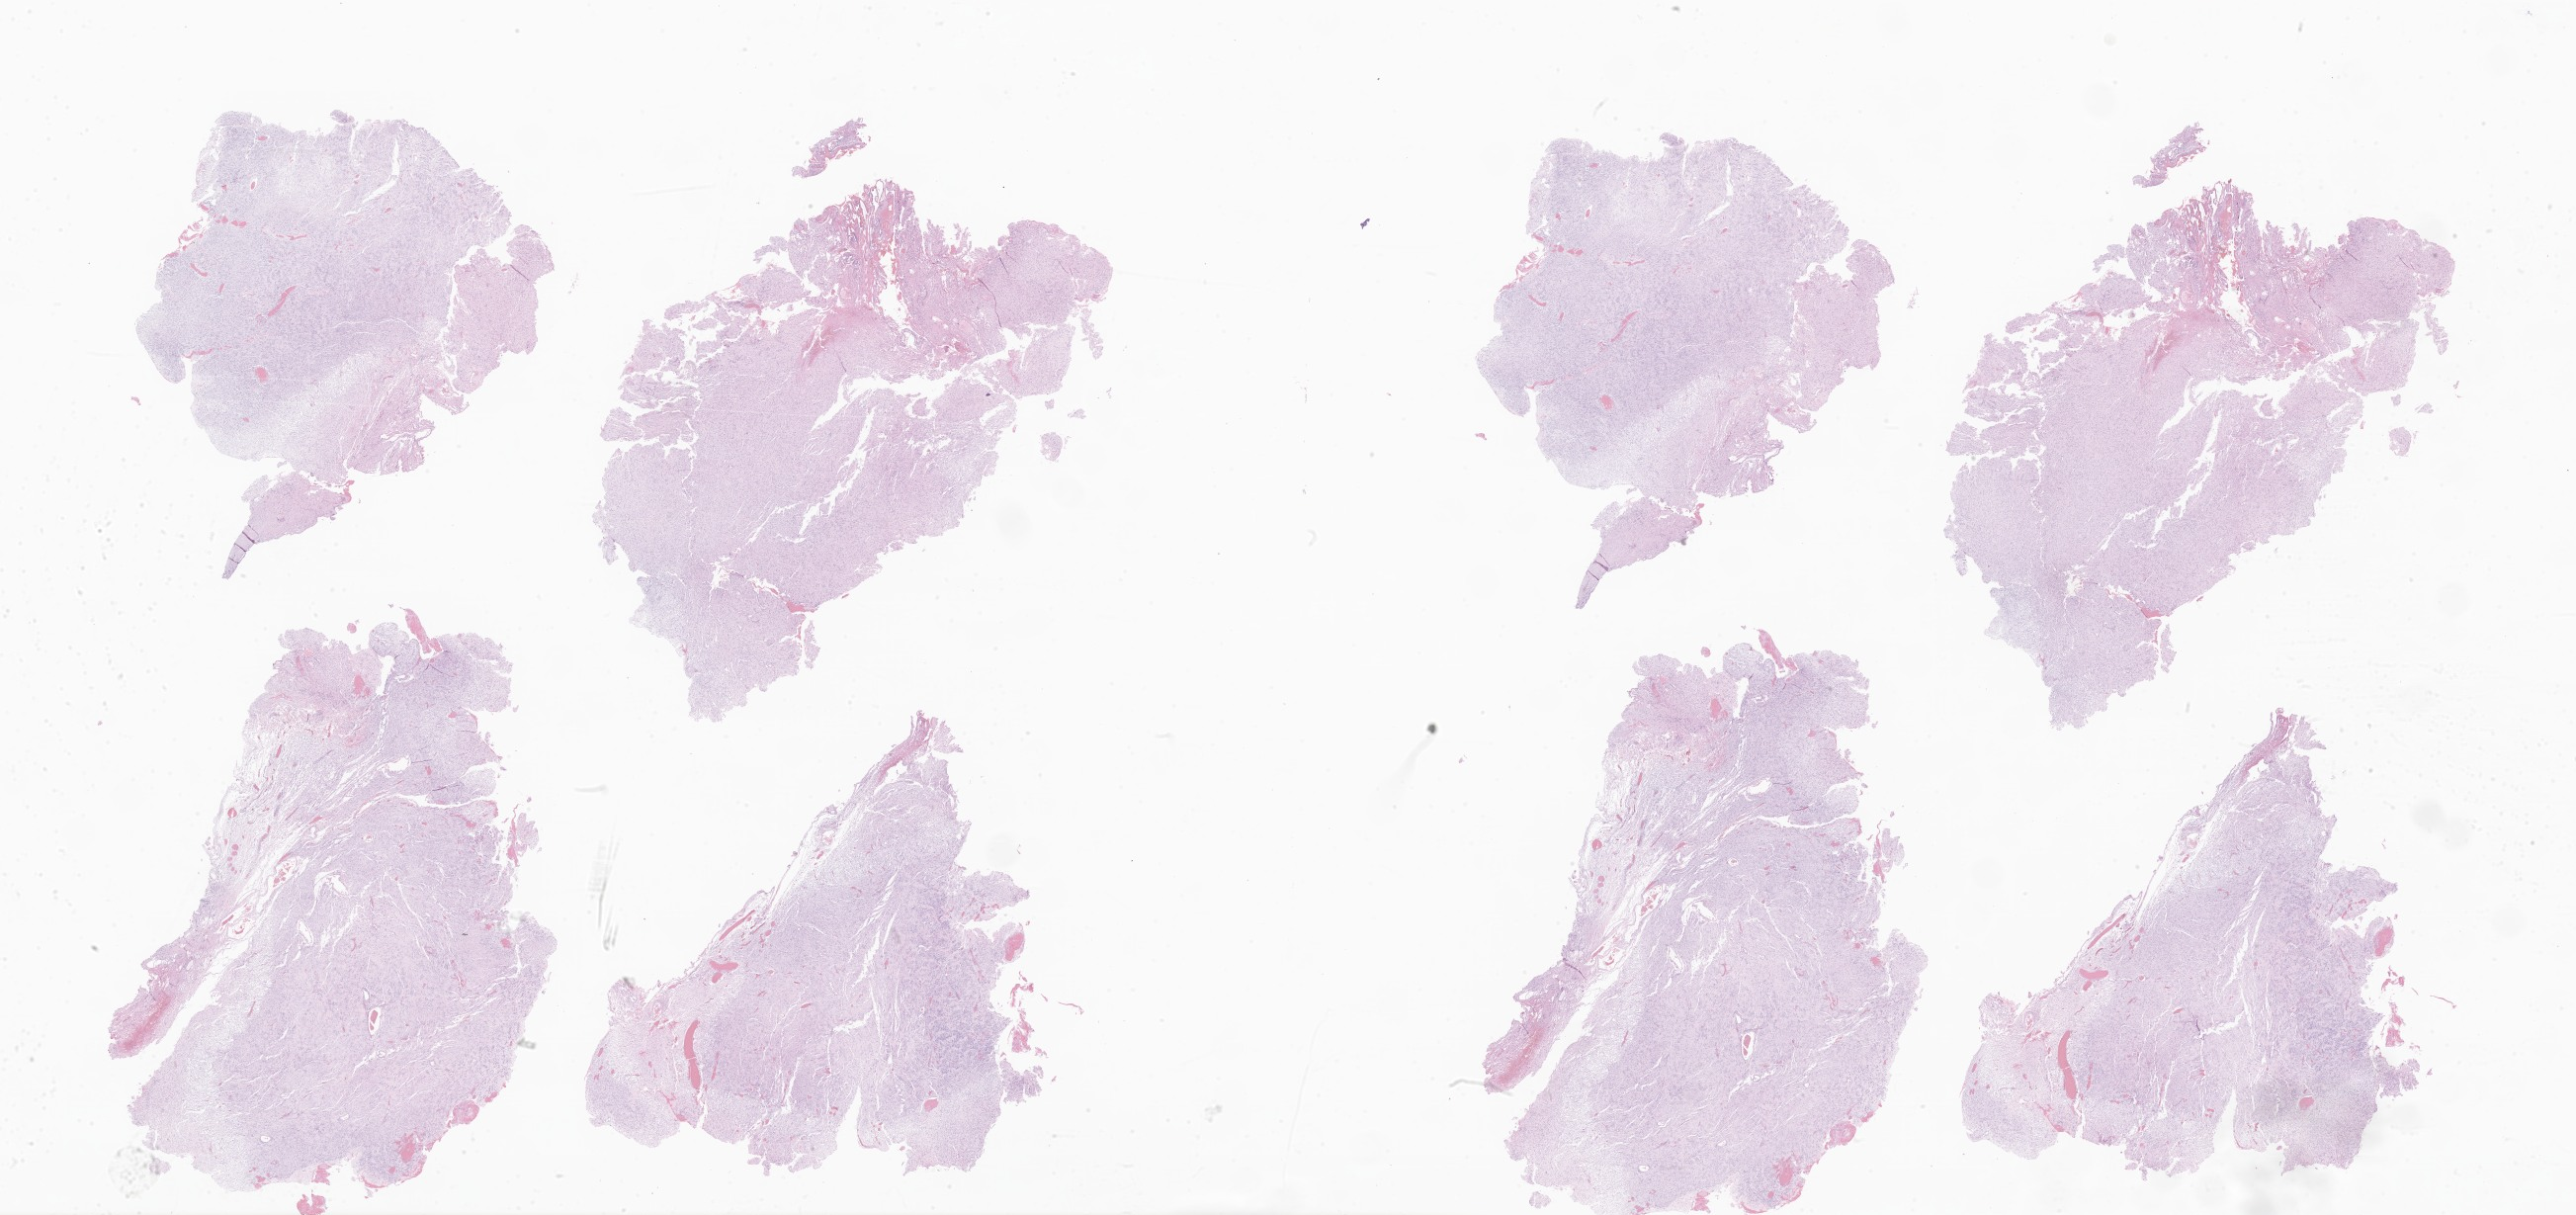
Digitized H&E-stained section of tumor tissue from the spinal cord — shown as a low-resolution overview of the whole scanned area (about 44.0 x 20.7 mm). FFPE section. Patient male; age 173 months (14 years 5 months).
- diagnosis (ICD-O-3 morphology term): Schwannoma, NOS